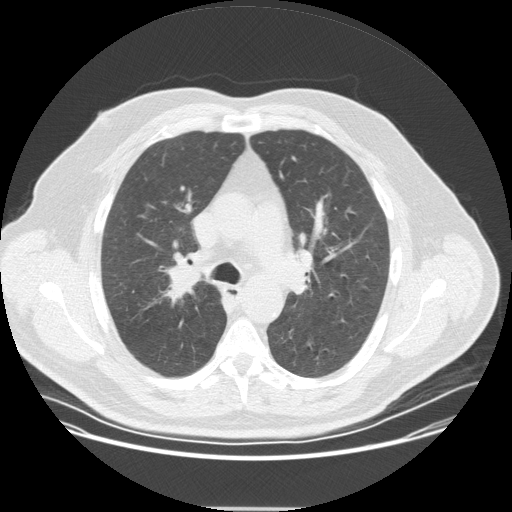
Chest CT (low-dose screening protocol), one axial image. Second screening round (one year after baseline). Lung window (W 1500 / L -600 HU). Slice 121 of 351 in the series. 512 × 512 image matrix. Male, age 57 years at enrolment. Current smoker at enrolment.
Expert-annotated lung lesion, bounding box [x1, y1, x2, y2] px = [150, 252, 211, 309]. The exam's reader record, not a measurement of the box and not confirmed to be the same lesion: non-calcified nodule or mass ≥4 mm, right upper lobe, 20 × 16 mm, spiculated (stellate) margins, soft tissue attenuation, pre-existing on the prior screen: no. Later outcome: lung cancer diagnosed 35 days after this screen — non-small cell carcinoma, right upper lobe, poorly differentiated (G3), stage IIA (AJCC 6th edition), 25 mm at pathology.